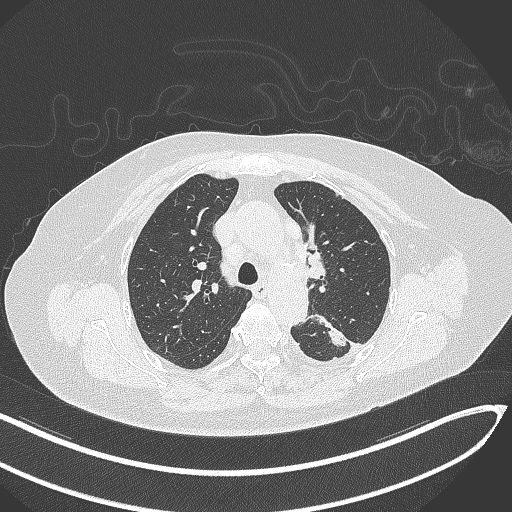
Chest CT, one axial slice. 120 kVp. Lung window (W 1500 / L -600 HU). 1 mm slice thickness. 512 × 512 image matrix, field of view 400 × 400 mm. Patient: female, 76 years. Case-level facts recorded for this patient, not image findings: clinical TNM (as recorded): T1c N0 M0.
Structures marked on this image (rectangle marked by the reading radiologist):
- lung tumour (recorded histology: adenocarcinoma): bounding box (x1, y1, x2, y2) in pixels: (315, 306, 355, 353)